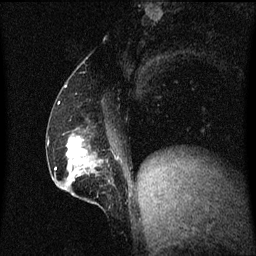
Breast MRI (dynamic contrast-enhanced), one sagittal slice; position 24 of 60 along the scan axis; dynamic contrast-enhanced series, image 2 of 3 at this slice position (ordered by acquisition); 1.5 T; TE 4.2 ms, TR 8.4 ms; 256 × 256 image matrix, field of view 200 × 200 mm. Female patient, age 52 years. From the clinical record (not read from this slice): setting: breast cancer imaged before/during neoadjuvant chemotherapy; receptor status: HER2-positive.
Structures marked on this image (semi-automatically segmented with operator editing):
- analysis volume of interest (the breast-tissue region the enhancement analysis was run in; not a lesion): bounding box [x1, y1, x2, y2] px = [62, 132, 116, 203]
- tumour enhancement mask (voxels above the 70 % enhancement threshold inside the analysis volume of interest): [67, 136, 88, 163]